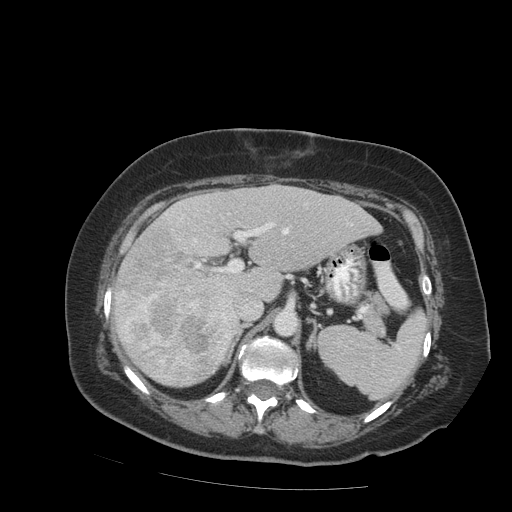
Contrast-enhanced abdominal CT (liver protocol), one axial slice. Position 52 of 99 along the scan axis. 140 kVp. Soft-tissue window (W 400 / L 40 HU). 512 × 512 image matrix. Case-level facts recorded for this patient, not image findings: diagnosis: hepatocellular carcinoma (patient treated with transarterial chemoembolisation; whether this scan precedes or follows treatment is not stated here); TNM stage (as recorded): Stage-IVB; Child-Pugh class: A; tumour differentiation: moderately differentiated.
Structures marked on this image (semi-automatically segmented with operator editing):
- liver parenchyma outside the tumour (the mass and vessels are separate outlines, so this box may not span the whole liver): bounding box <112,184,381,386> (left, top, right, bottom; pixels)
- mass: <111,222,232,386>
- liver vessels: <166,213,289,320>